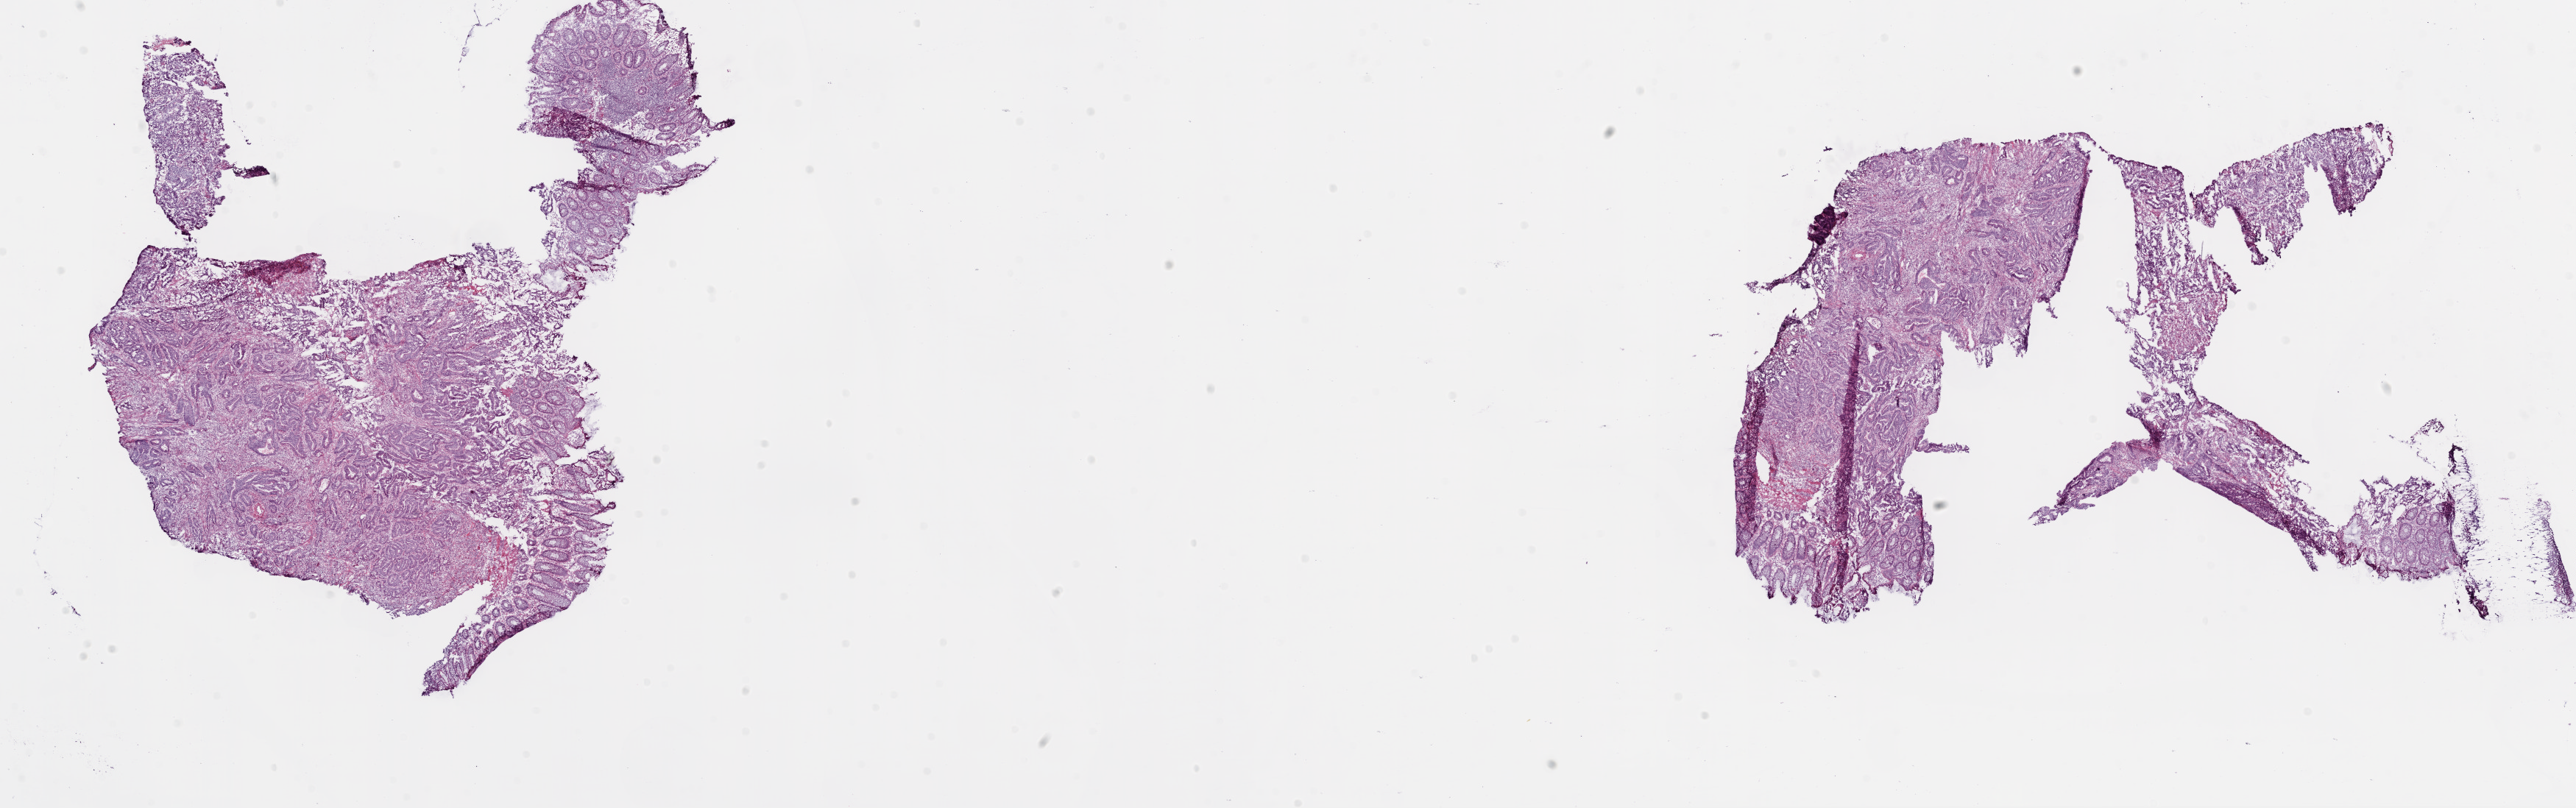
H&E whole-slide image — shown as a low-resolution overview of the whole scanned area (about 28.1 x 8.8 mm, acquisition: 20x scan). Frozen section from the bottom of the tissue portion. Rectum, primary tumour sample. Male patient; age at initial diagnosis 64 years. Slide review estimates, as recorded: tumour cells 72%, tumour nuclei 75%, normal cells 15%, stromal cells 10%, necrosis 3%.
TNM: T2 N0 M0. AJCC pathologic stage: I (6th edition). Pathologic diagnosis: Adenocarcinoma, NOS.